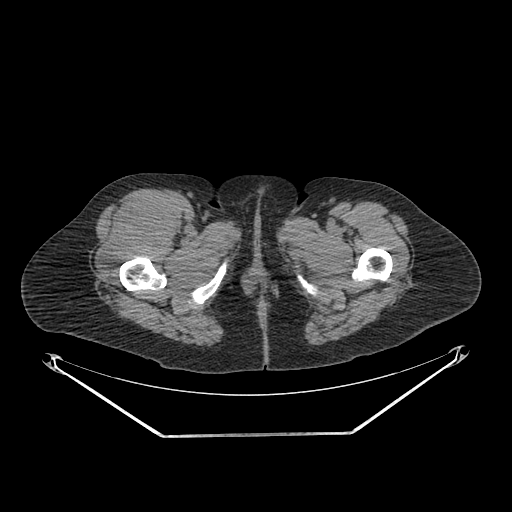
CT of an extremity soft-tissue mass (from a PET/CT study), one axial slice. Slice 277 of 311 in the series (ordered by position). 140 kVp. Soft-tissue window (W 400 / L 40 HU). 3.75 mm slice thickness. 512 × 512 image matrix. Female patient. Case-level facts recorded for this patient, not image findings: histological type: pleiomorphic undifferentiated sarcoma; grade: high; site of the primary tumour: right quadricep.
Structures marked on this image (expert contour drawn on MRI and transferred to this co-registered scan by the dataset authors):
- tumour plus oedema (research contour): bounding box <98,198,172,273> (left, top, right, bottom; pixels)
- tumour (research contour): <98,198,172,273>